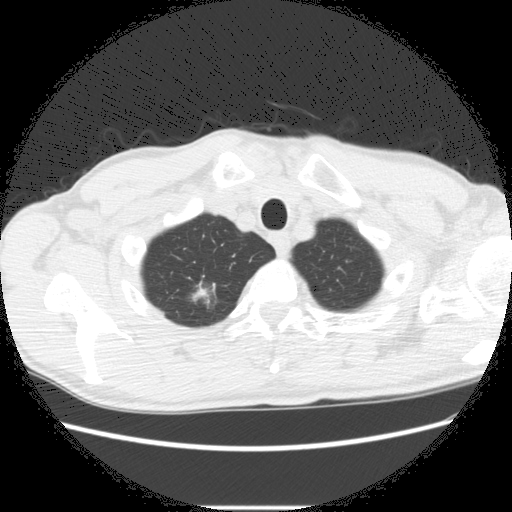
Low-dose screening chest CT, one axial slice; position 257 of 282 along the scan axis; reconstruction kernel STANDARD; lung window (W 1500 / L -600 HU); 512 × 512 image matrix.
Annotated regions visible in this slice (outlined manually by an expert reader):
- lesion 2 (nodule, upper lobe of right lung): bounding box <190,282,213,305> (left, top, right, bottom; pixels)